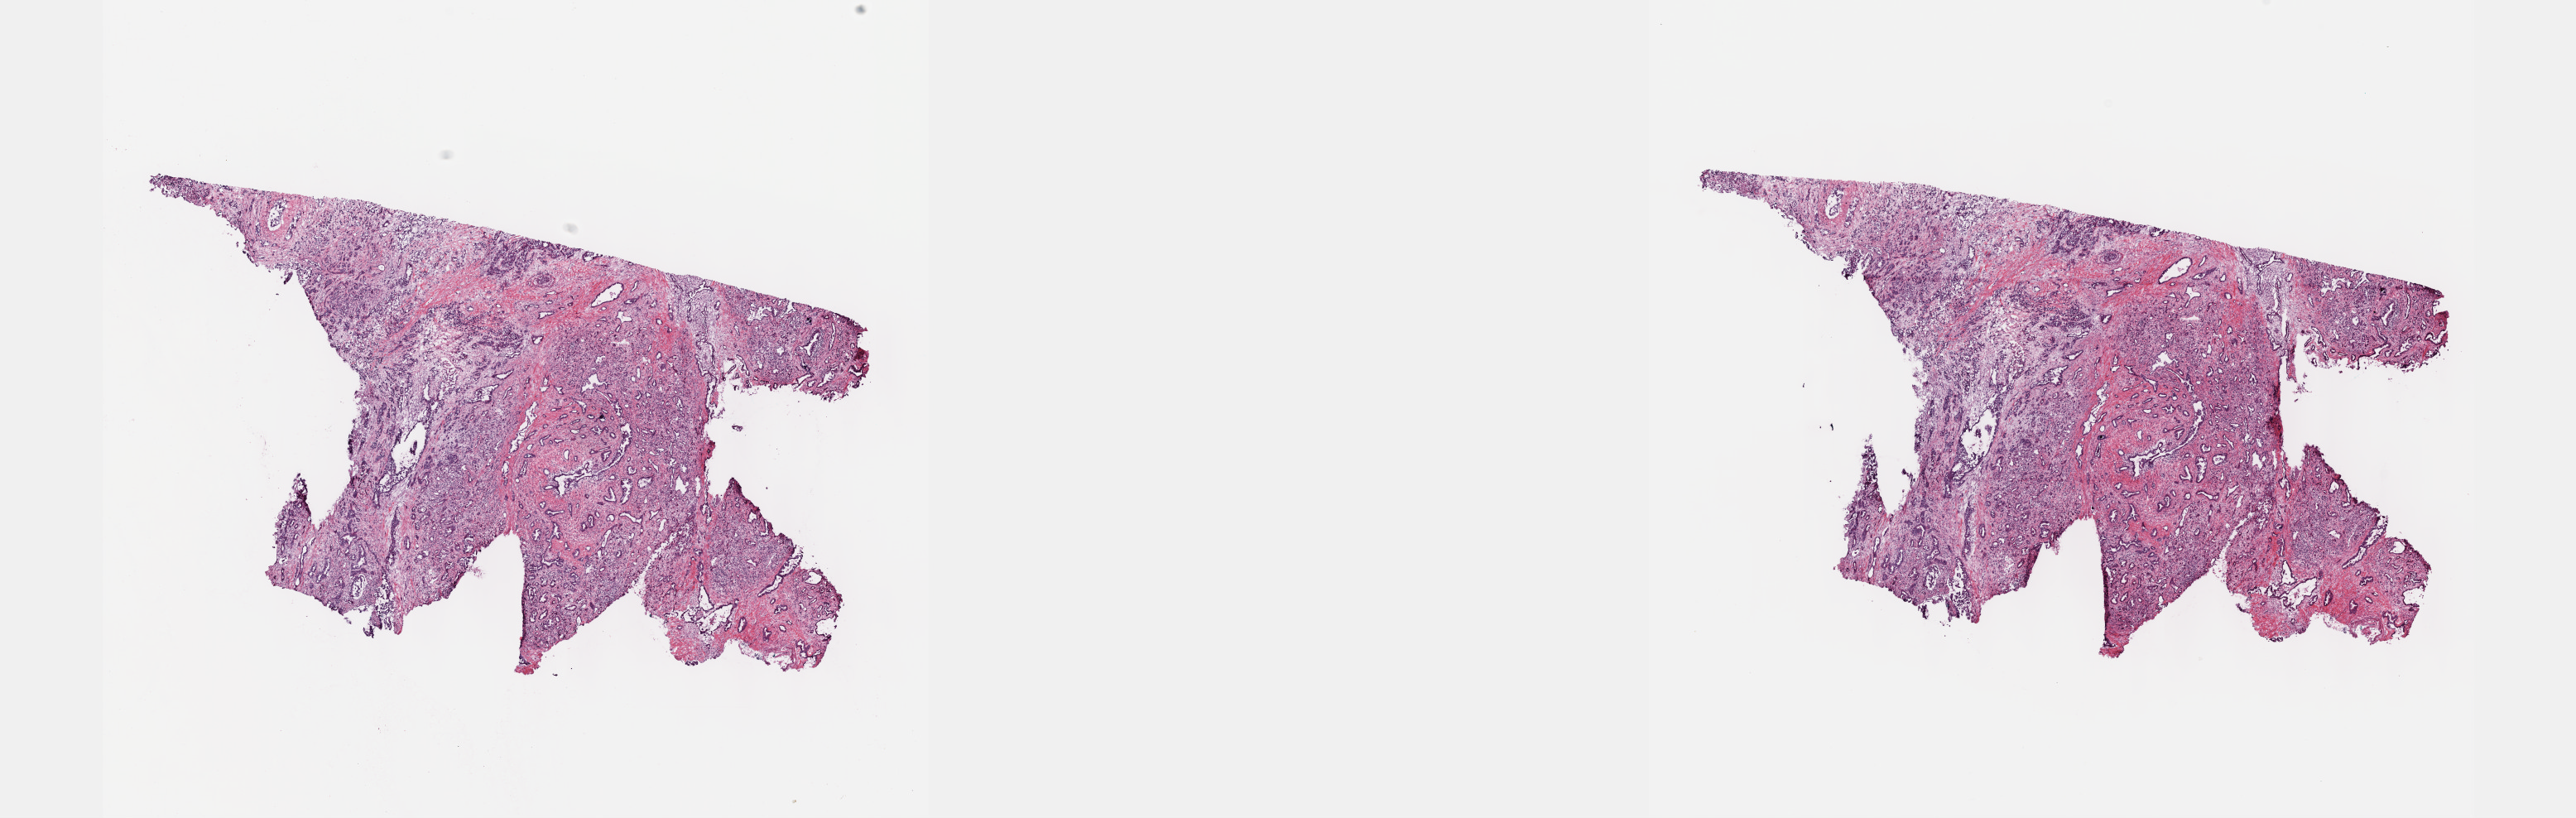
Digitized H&E tissue section (whole slide), a low-resolution overview of the entire scanned area, about 25.1 x 8.0 mm (from a 40x scan); frozen section from the top of the tissue portion; sample: primary tumour, pancreas. Male, age 57 years at initial diagnosis. Histologic grade: G2 (moderately differentiated). Composition of this section per pathologist review: tumour cells 50%, tumour nuclei 60%, normal cells 0%, stromal cells 50%, necrosis 0%. Infiltration values recorded for this section: lymphocyte infiltration 0%, monocyte infiltration 0%, neutrophil infiltration 0%.
AJCC pathologic stage: IIB (7th edition). Diagnosis: Infiltrating duct carcinoma, NOS (head of pancreas).